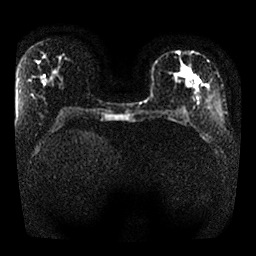
Breast MRI, one axial slice; slice 12 of 25 in the series (ordered by position); diffusion-weighted series; image 2 of 4 stored at this slice position (different b-values; order by instance number); 1.5 T; 4 mm slice thickness; 256 × 256 image matrix, field of view 330 × 330 mm. Female patient.
Structures marked on this image (expert manual segmentation):
- tumour on diffusion-weighted imaging: bounding box [x1, y1, x2, y2] px = [171, 72, 199, 98]